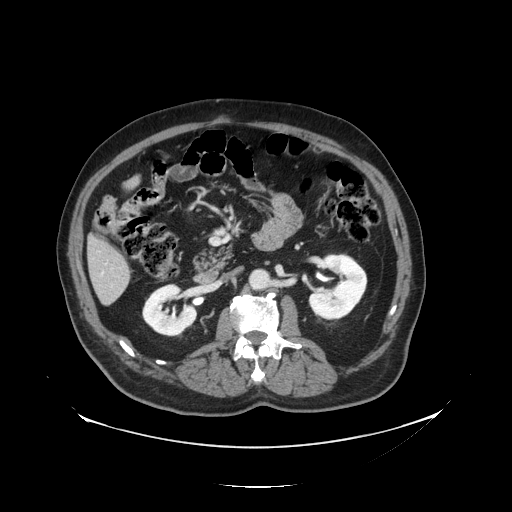
Contrast-enhanced abdominal CT, one axial slice; slice 47 of 138 in the series (ordered by position); 120 kVp; intravenous contrast given; soft-tissue window (W 400 / L 40 HU); 2.5 mm slice thickness; 512 × 512 image matrix. Male patient, age 77 years. From the clinical record (not read from this slice): diagnosis: colorectal cancer liver metastases, imaged before liver resection; multiple liver metastases: no; largest metastasis: 1.5 cm; chemotherapy before resection: no.
Outlined on this slice (outlined manually by an expert reader):
- liver: bounding box <89,239,131,305> (left, top, right, bottom; pixels)
- planned liver remnant (the part of the liver to remain after resection): <89,239,129,278>